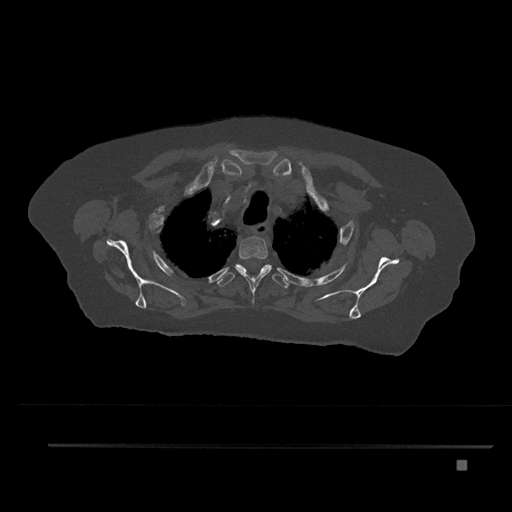
CT including the spine, one axial slice. Position 656 of 797 along the scan axis. Reconstruction kernel Br40s/3. 120 kVp. Bone window (W 1800 / L 400 HU). 0.5 mm slice thickness. 512 × 512 image matrix, field of view 437 × 437 mm. Patient: female, 76 years. Case-level facts recorded for this patient, not image findings: primary cancer: lung.
Annotated regions visible in this slice (semi-automatically segmented with operator editing):
- T2 vertebra: bounding box (x1, y1, x2, y2) in pixels: (235, 231, 272, 303)
- T3 vertebra: (217, 264, 288, 288)